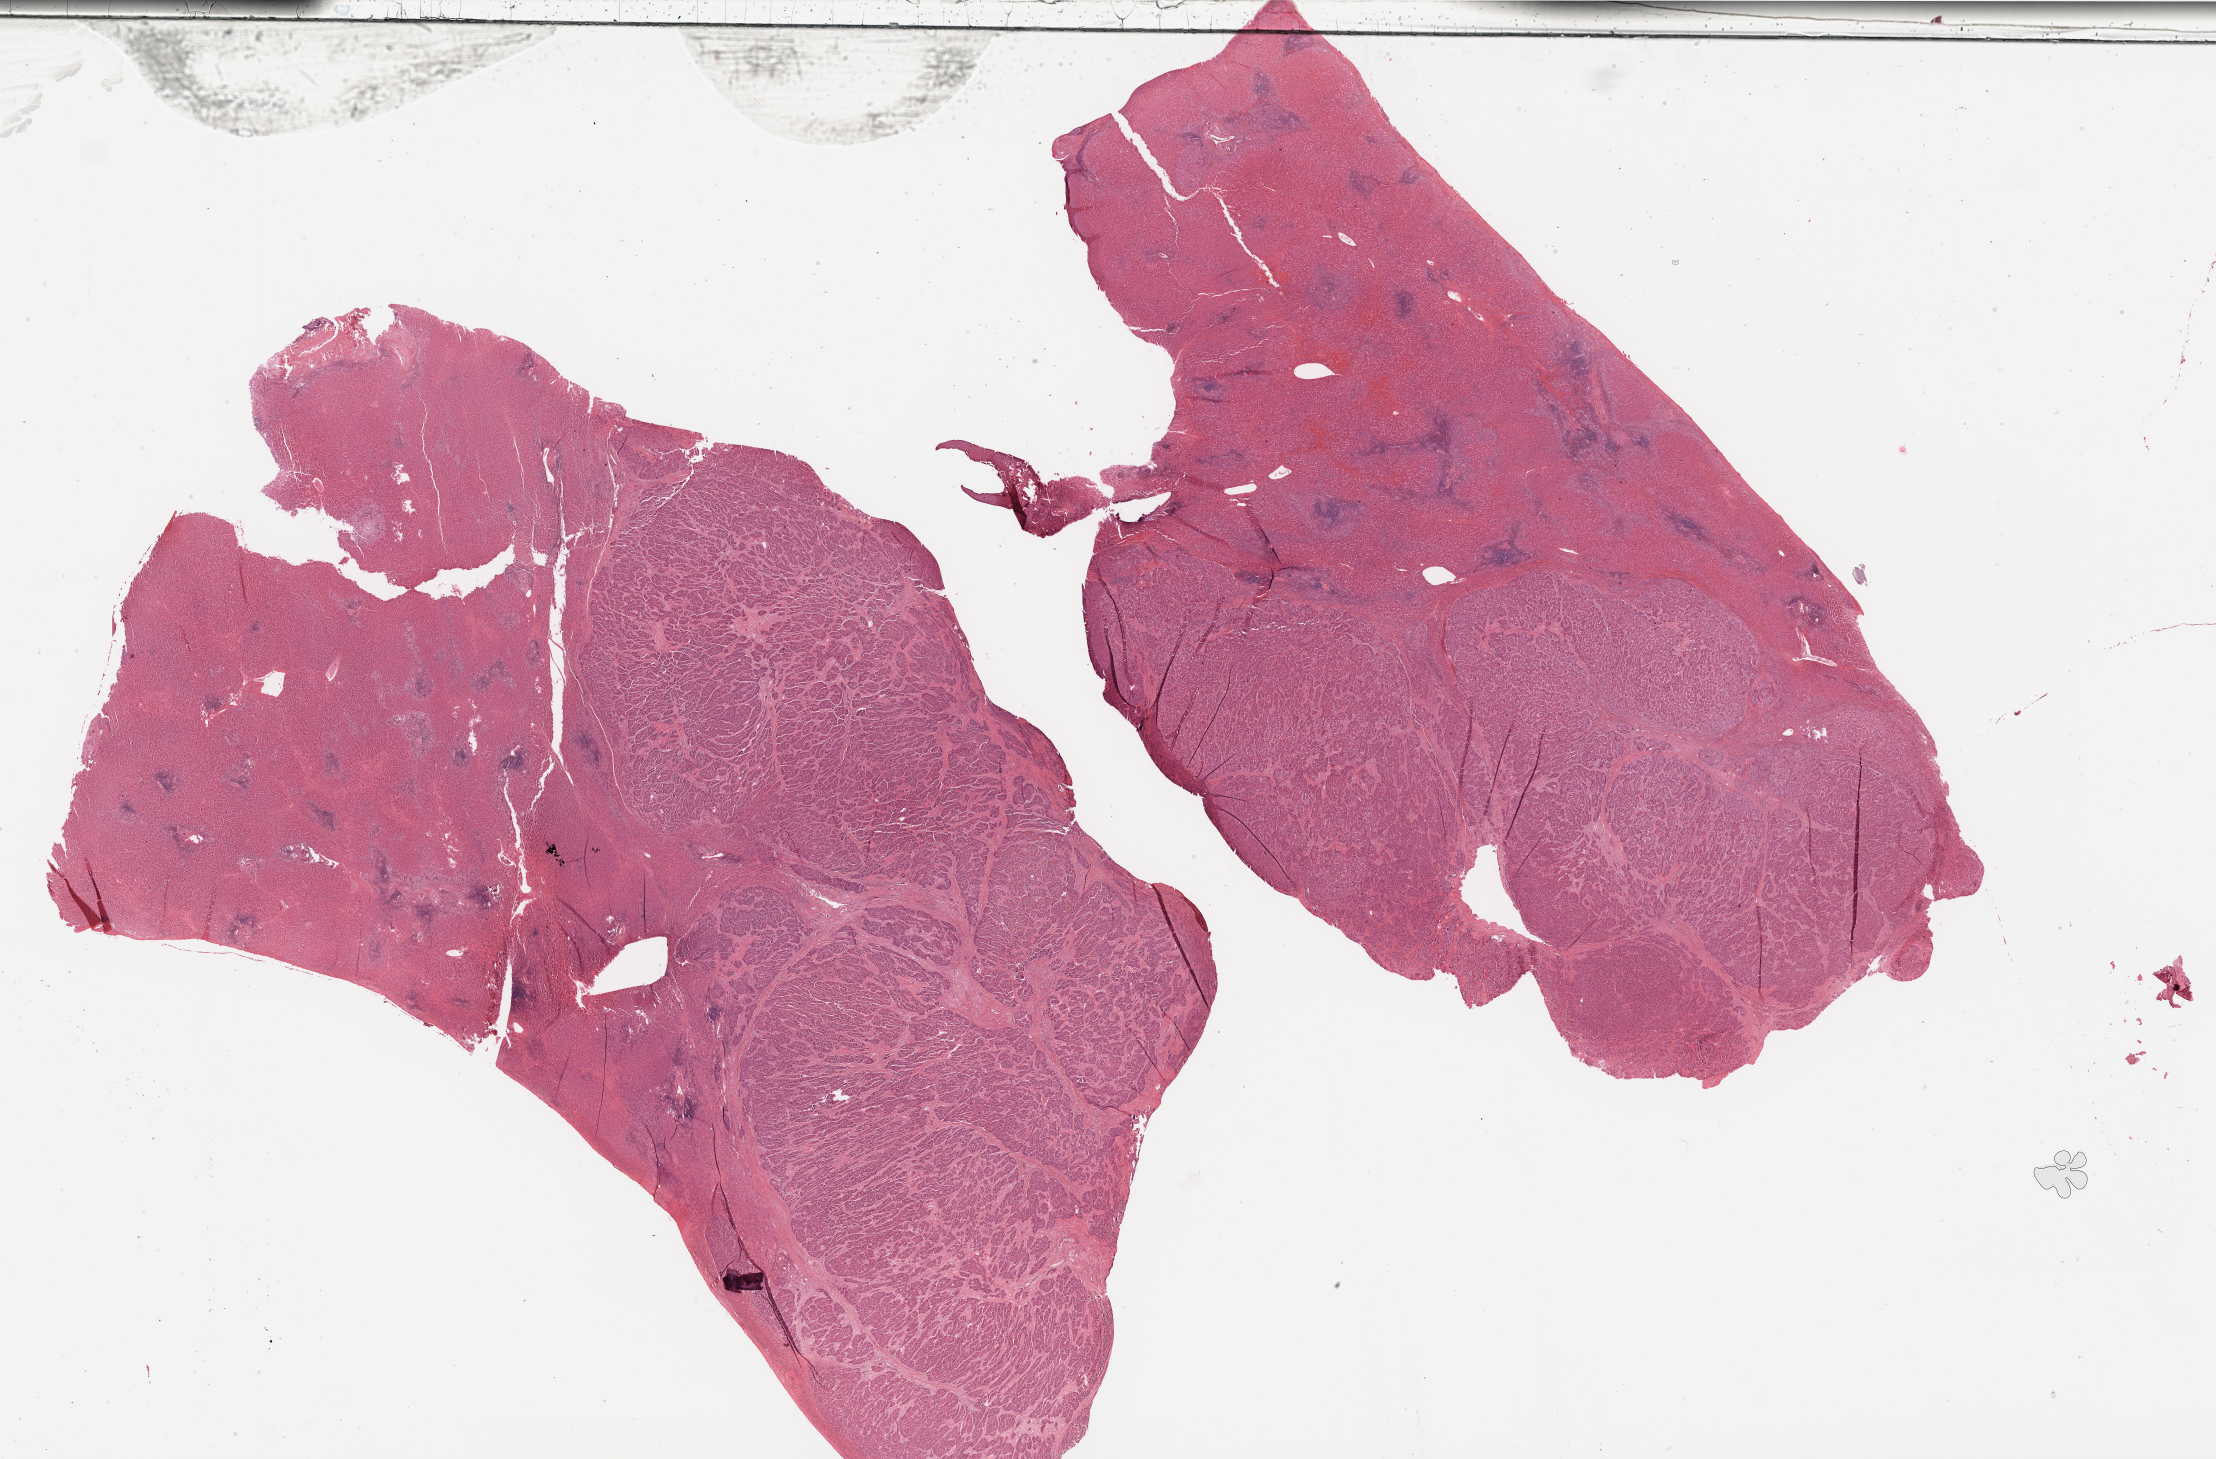
Whole-slide histology image, H&E-stained, whole scanned area (about 35.9 x 23.6 mm) shown as a low-resolution overview. FFPE section. Liver, primary tumour sample. Male patient; age at initial diagnosis 40 years. Histologic grade: G3 (poorly differentiated).
AJCC pathologic stage: IV. Histologic diagnosis: Hepatocellular carcinoma, NOS. TNM: T3a N0 M1.